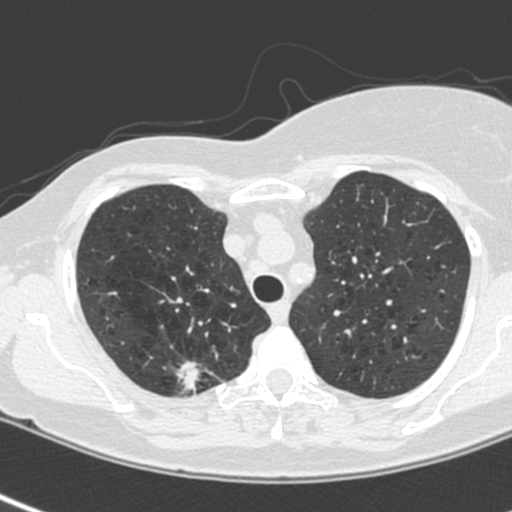
Axial slice from a low-dose chest CT screening exam. First (baseline) screen. Lung window (W 1500 / L -600 HU). 1.3 mm slice thickness. 512 × 512 image matrix. Female participant, aged 64 years at enrolment. Current smoker at enrolment.
- Expert reader's lesion annotation, bounding box <165,354,220,404> (left, top, right, bottom; pixels).
- Reader record for this screening exam (exam-level; its link to the box is not recorded): non-calcified nodule or mass ≥4 mm, right upper lobe, 13 × 10 mm, spiculated (stellate) margins, soft tissue attenuation.
- Official screen result: positive, change unspecified: nodule(s) >= 4 mm or enlarging nodule(s), mass(es), or other non-specific abnormalities suspicious for lung cancer.
- Later outcome: lung cancer diagnosed 21 days after this screen — adenocarcinoma, NOS, right upper lobe, poorly differentiated (G3), stage IIIB (AJCC 6th edition), 20 mm at pathology.